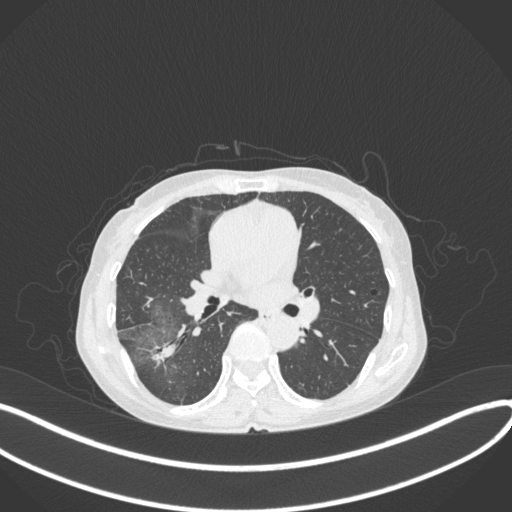
Chest CT, one axial slice. Slice 213 of 379 in the series (ordered by position). Reconstruction kernel B31f. Lung window (W 1500 / L -600 HU). 1 mm slice thickness. 512 × 512 image matrix, field of view 400 × 400 mm. Patient: female, 69 years. Case-level facts recorded for this patient, not image findings: clinical TNM (as recorded): T1b N0 M0; histopathological grade: G2-3.
Annotated regions visible in this slice (bounding box drawn by a radiologist):
- lung tumour (recorded histology: adenocarcinoma): bounding box [x1, y1, x2, y2] px = [147, 339, 182, 368]